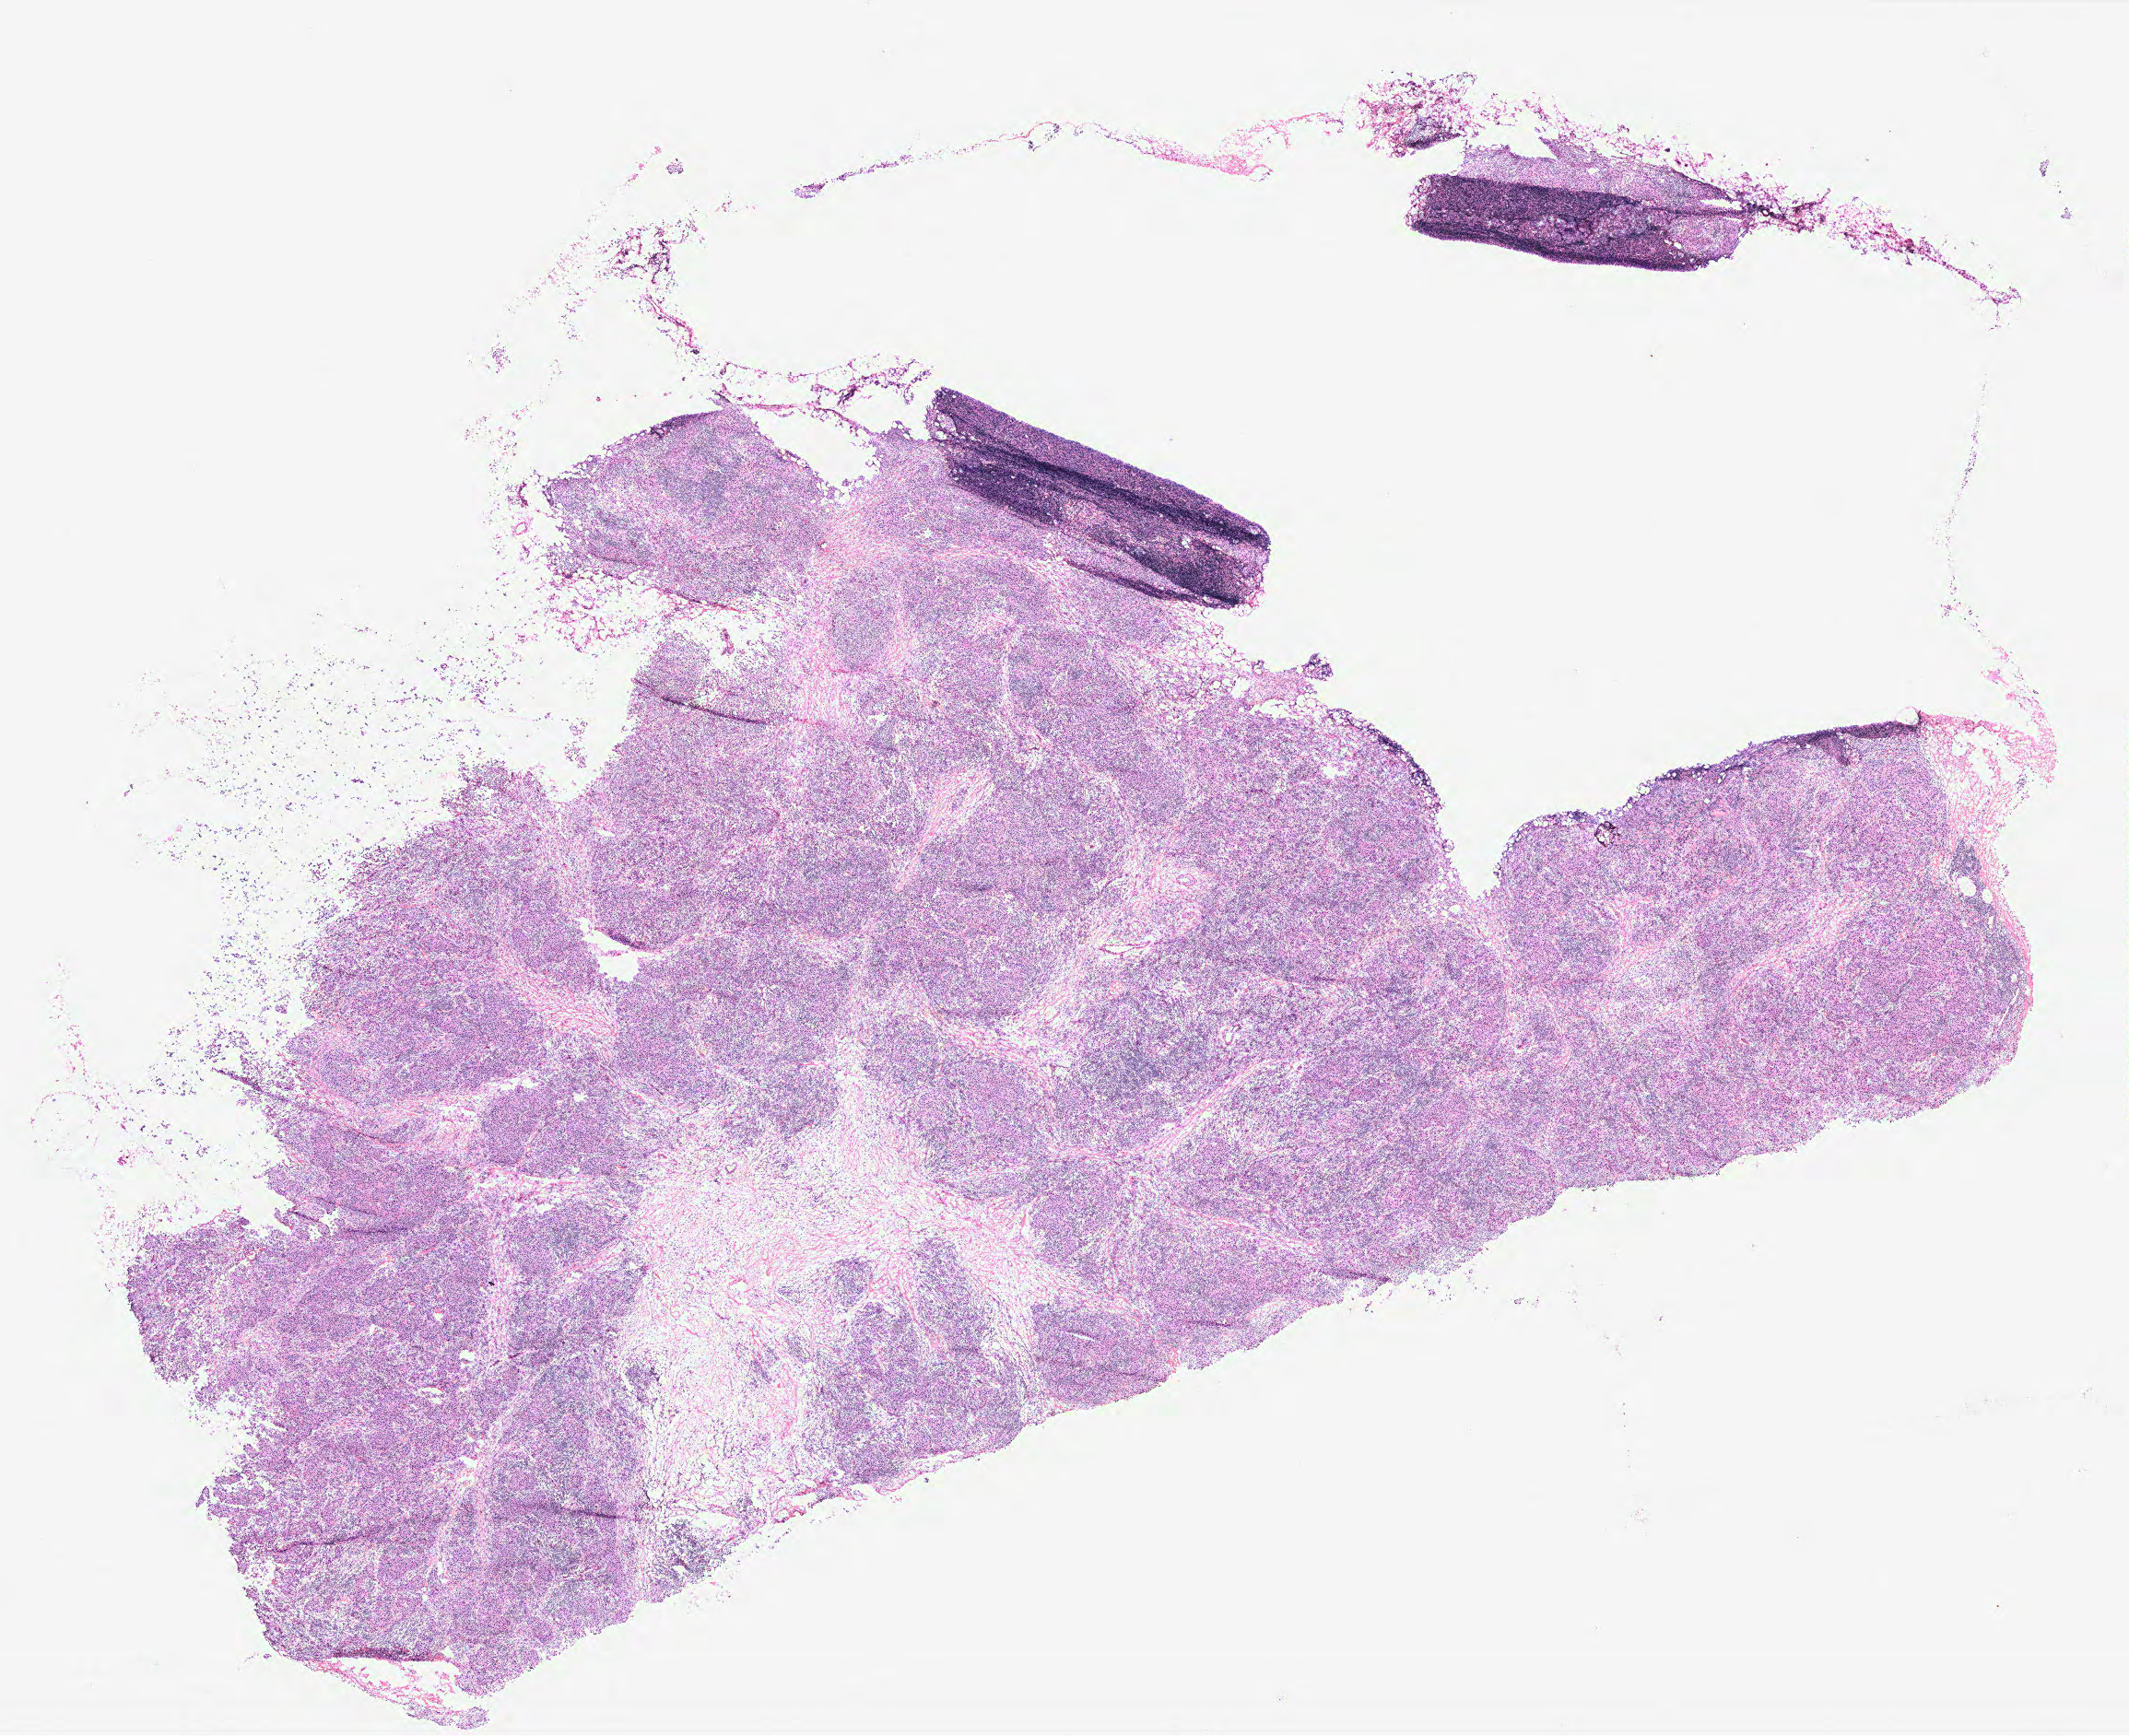
H&E-stained whole-slide image, whole scanned area (about 18.5 x 15.1 mm, from a 40x scan) shown as a low-resolution overview; tumour tissue sample, breast. 64-year-old female patient.
Histologic diagnosis: Infiltrating duct carcinoma, NOS. AJCC pathologic stage: IIIA.